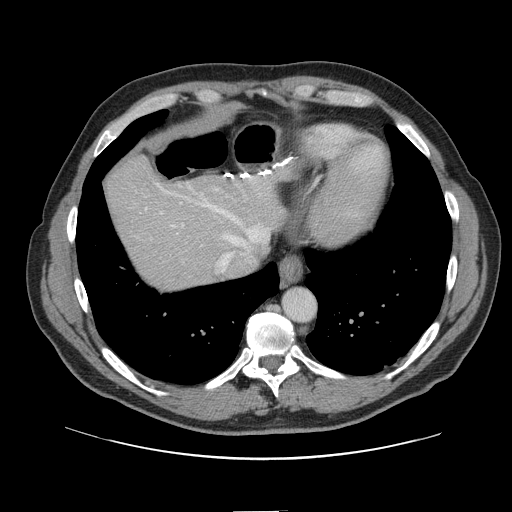
Contrast-enhanced abdominal CT, one axial slice. 120 kVp. Intravenous contrast given. Soft-tissue window (W 400 / L 40 HU). 512 × 512 image matrix, field of view 412 × 412 mm. Male patient, age 66 years. From the clinical record (not read from this slice): diagnosis: colorectal cancer liver metastases, imaged before liver resection; multiple liver metastases: no; largest metastasis: 3.5 cm; disease in both lobes: no.
Outlined on this slice (outlined manually by an expert reader):
- hepatic veins: box from (x=146, y=183) to (x=271, y=273) px
- liver: (x=106, y=158)–(x=284, y=290)
- planned liver remnant (the part of the liver to remain after resection): (x=106, y=158)–(x=285, y=287)